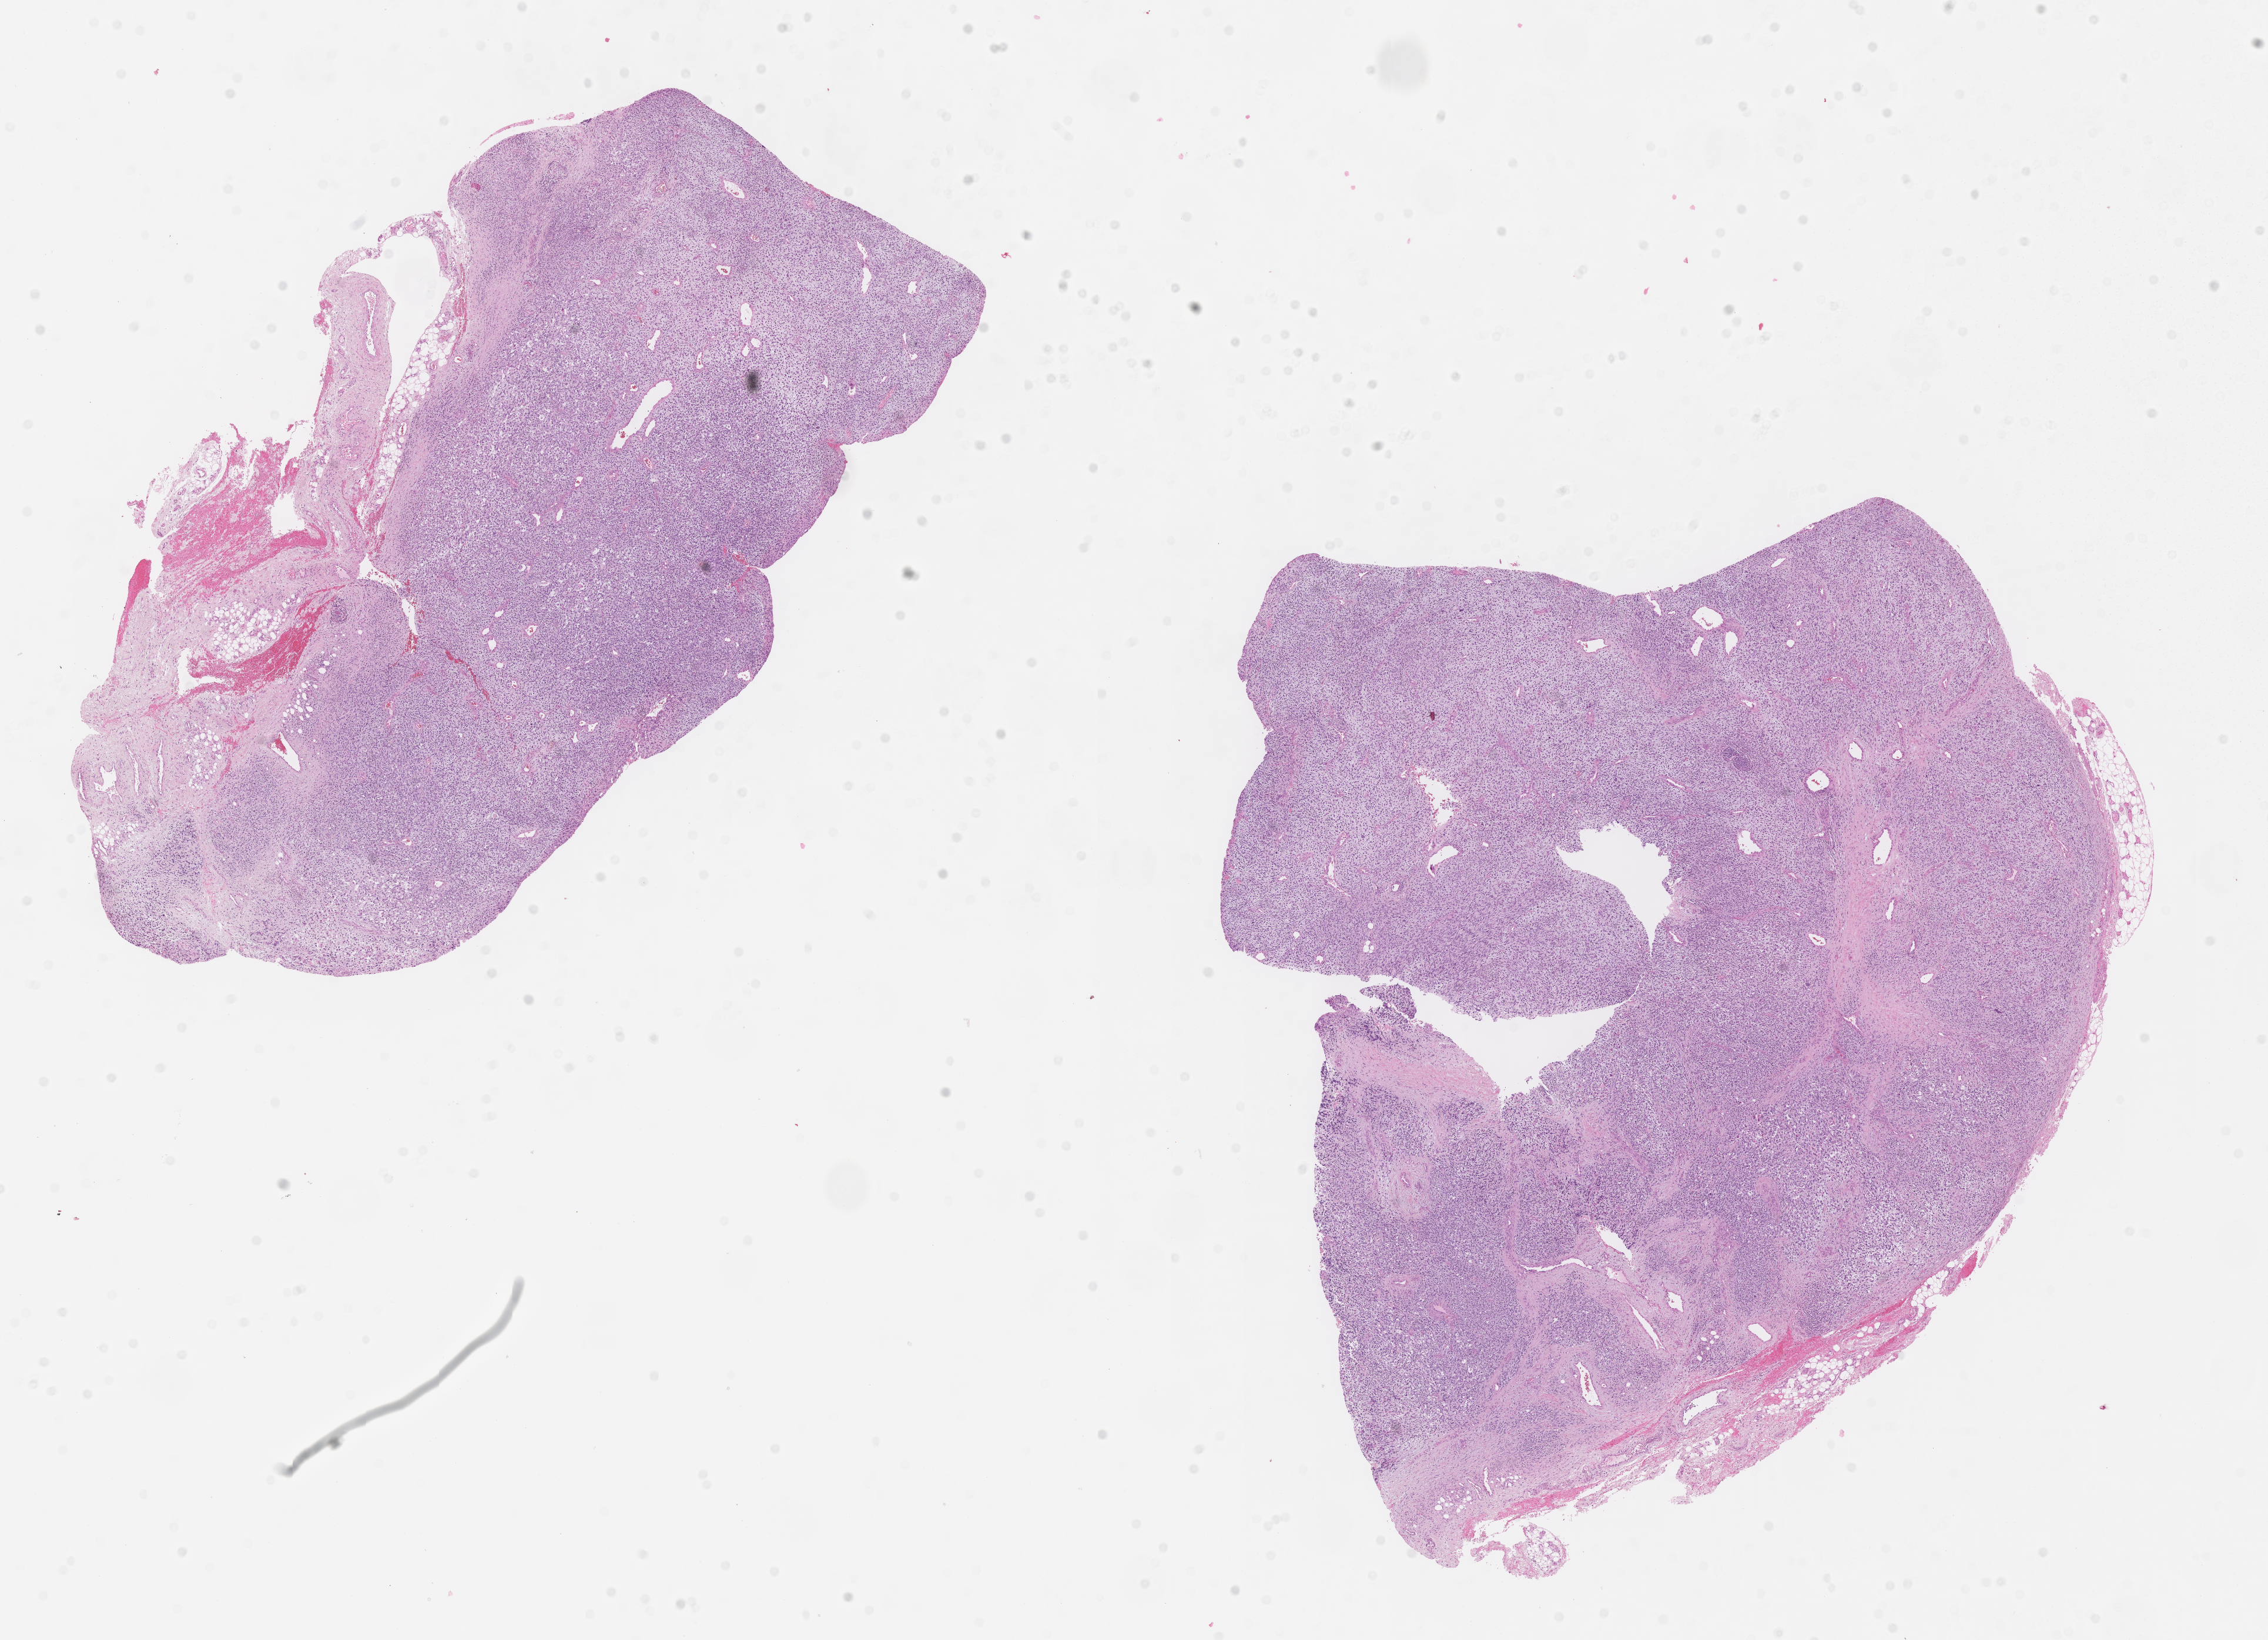
Whole-slide image, H&E stain of tumor tissue, a low-resolution overview of the entire scanned area, about 15.6 x 11.3 mm. Formalin-fixed paraffin-embedded section. Site: orbit, left. Patient: male, age 6.6 years at diagnosis.
Stage (as recorded): 1. Diagnosis: rhabdomyosarcoma; histological classification: embryonal rhabdomyosarcoma. Metastatic status at presentation (as recorded): non-metastatic.